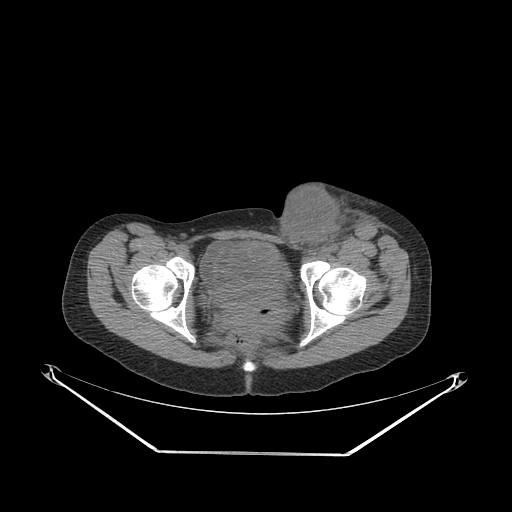
CT of an extremity soft-tissue mass (from a PET/CT study), one axial slice; slice 71 of 267 in the series (ordered by position); soft-tissue window (W 400 / L 40 HU); 512 × 512 image matrix, field of view 500 × 500 mm. Female patient. From the clinical record (not read from this slice): histological type: leiomyosarcoma; grade: high; site of the primary tumour: groin.
Structures marked on this image (expert contour drawn on MRI and transferred to this co-registered scan by the dataset authors):
- gross tumour volume including surrounding oedema: box from (x=272, y=189) to (x=385, y=264) px
- gross tumour volume (mass): (x=272, y=190)–(x=346, y=252)